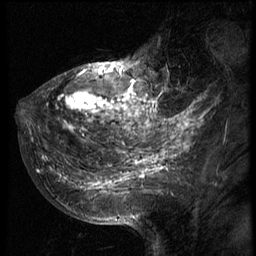
Breast MRI (dynamic contrast-enhanced), one sagittal slice. Slice 24 of 66 in the series (ordered by position). 3 images stored at this slice position (order not interpretable as contrast timing). 1.5 T. TE 4.2 ms, TR 8.9 ms. 2.5 mm slice thickness. 256 × 256 image matrix, field of view 200 × 200 mm. Female patient, age 39 years. Case-level facts recorded for this patient, not image findings: setting: breast cancer imaged before/during neoadjuvant chemotherapy; receptor status: HER2-positive.
Outlined on this slice (semi-automatic segmentation, software-assisted and operator-edited):
- analysis volume of interest (the breast-tissue region the enhancement analysis was run in; not a lesion): box from (x=29, y=44) to (x=166, y=196) px
- tumour enhancement mask (voxels above the 140 % enhancement threshold inside the analysis volume of interest): (x=29, y=62)–(x=166, y=189)